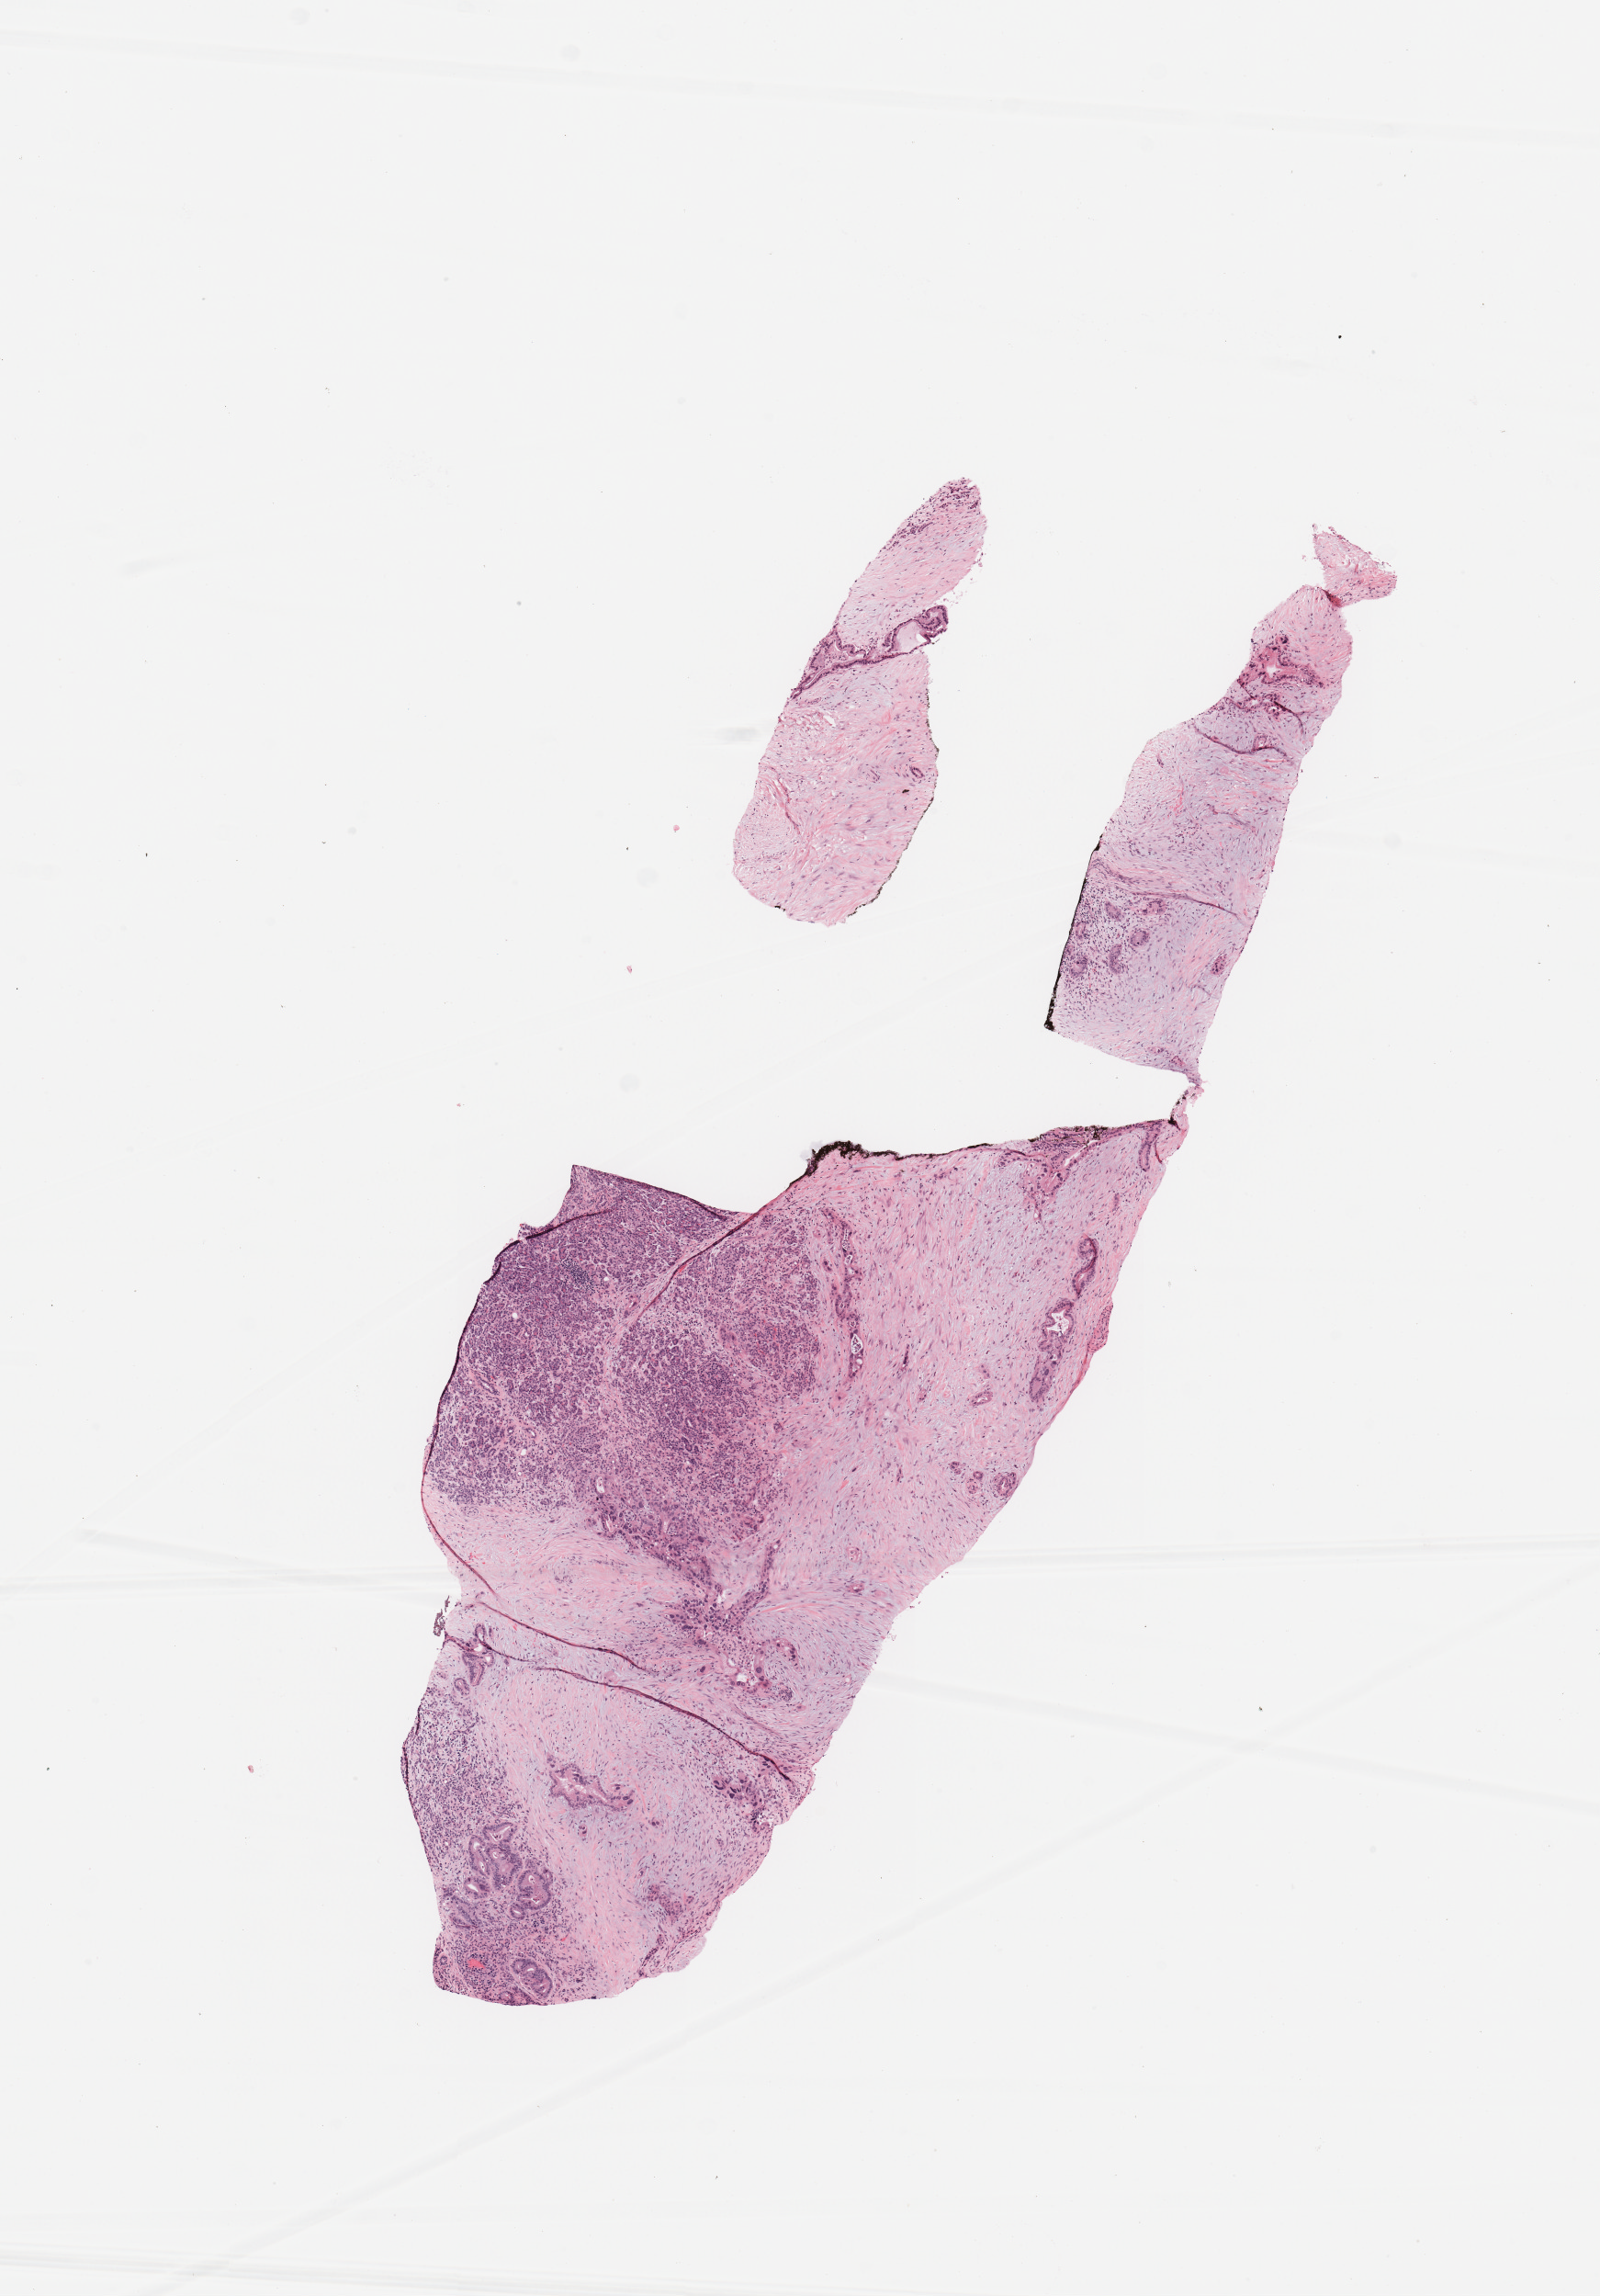
Hematoxylin and eosin (H&E) stained whole-slide image, shown as a low-resolution overview of the whole scanned area (about 6.9 x 9.9 mm, from a 20x scan), tumour tissue sample, sampled site: pancreas. Female, 36 y/o. Histologic grade: G2 (moderately differentiated). Composition of this section per pathologist review: tumour nuclei 10%, necrosis 0%.
* AJCC pathologic stage: III
* diagnosis: Infiltrating duct carcinoma, NOS